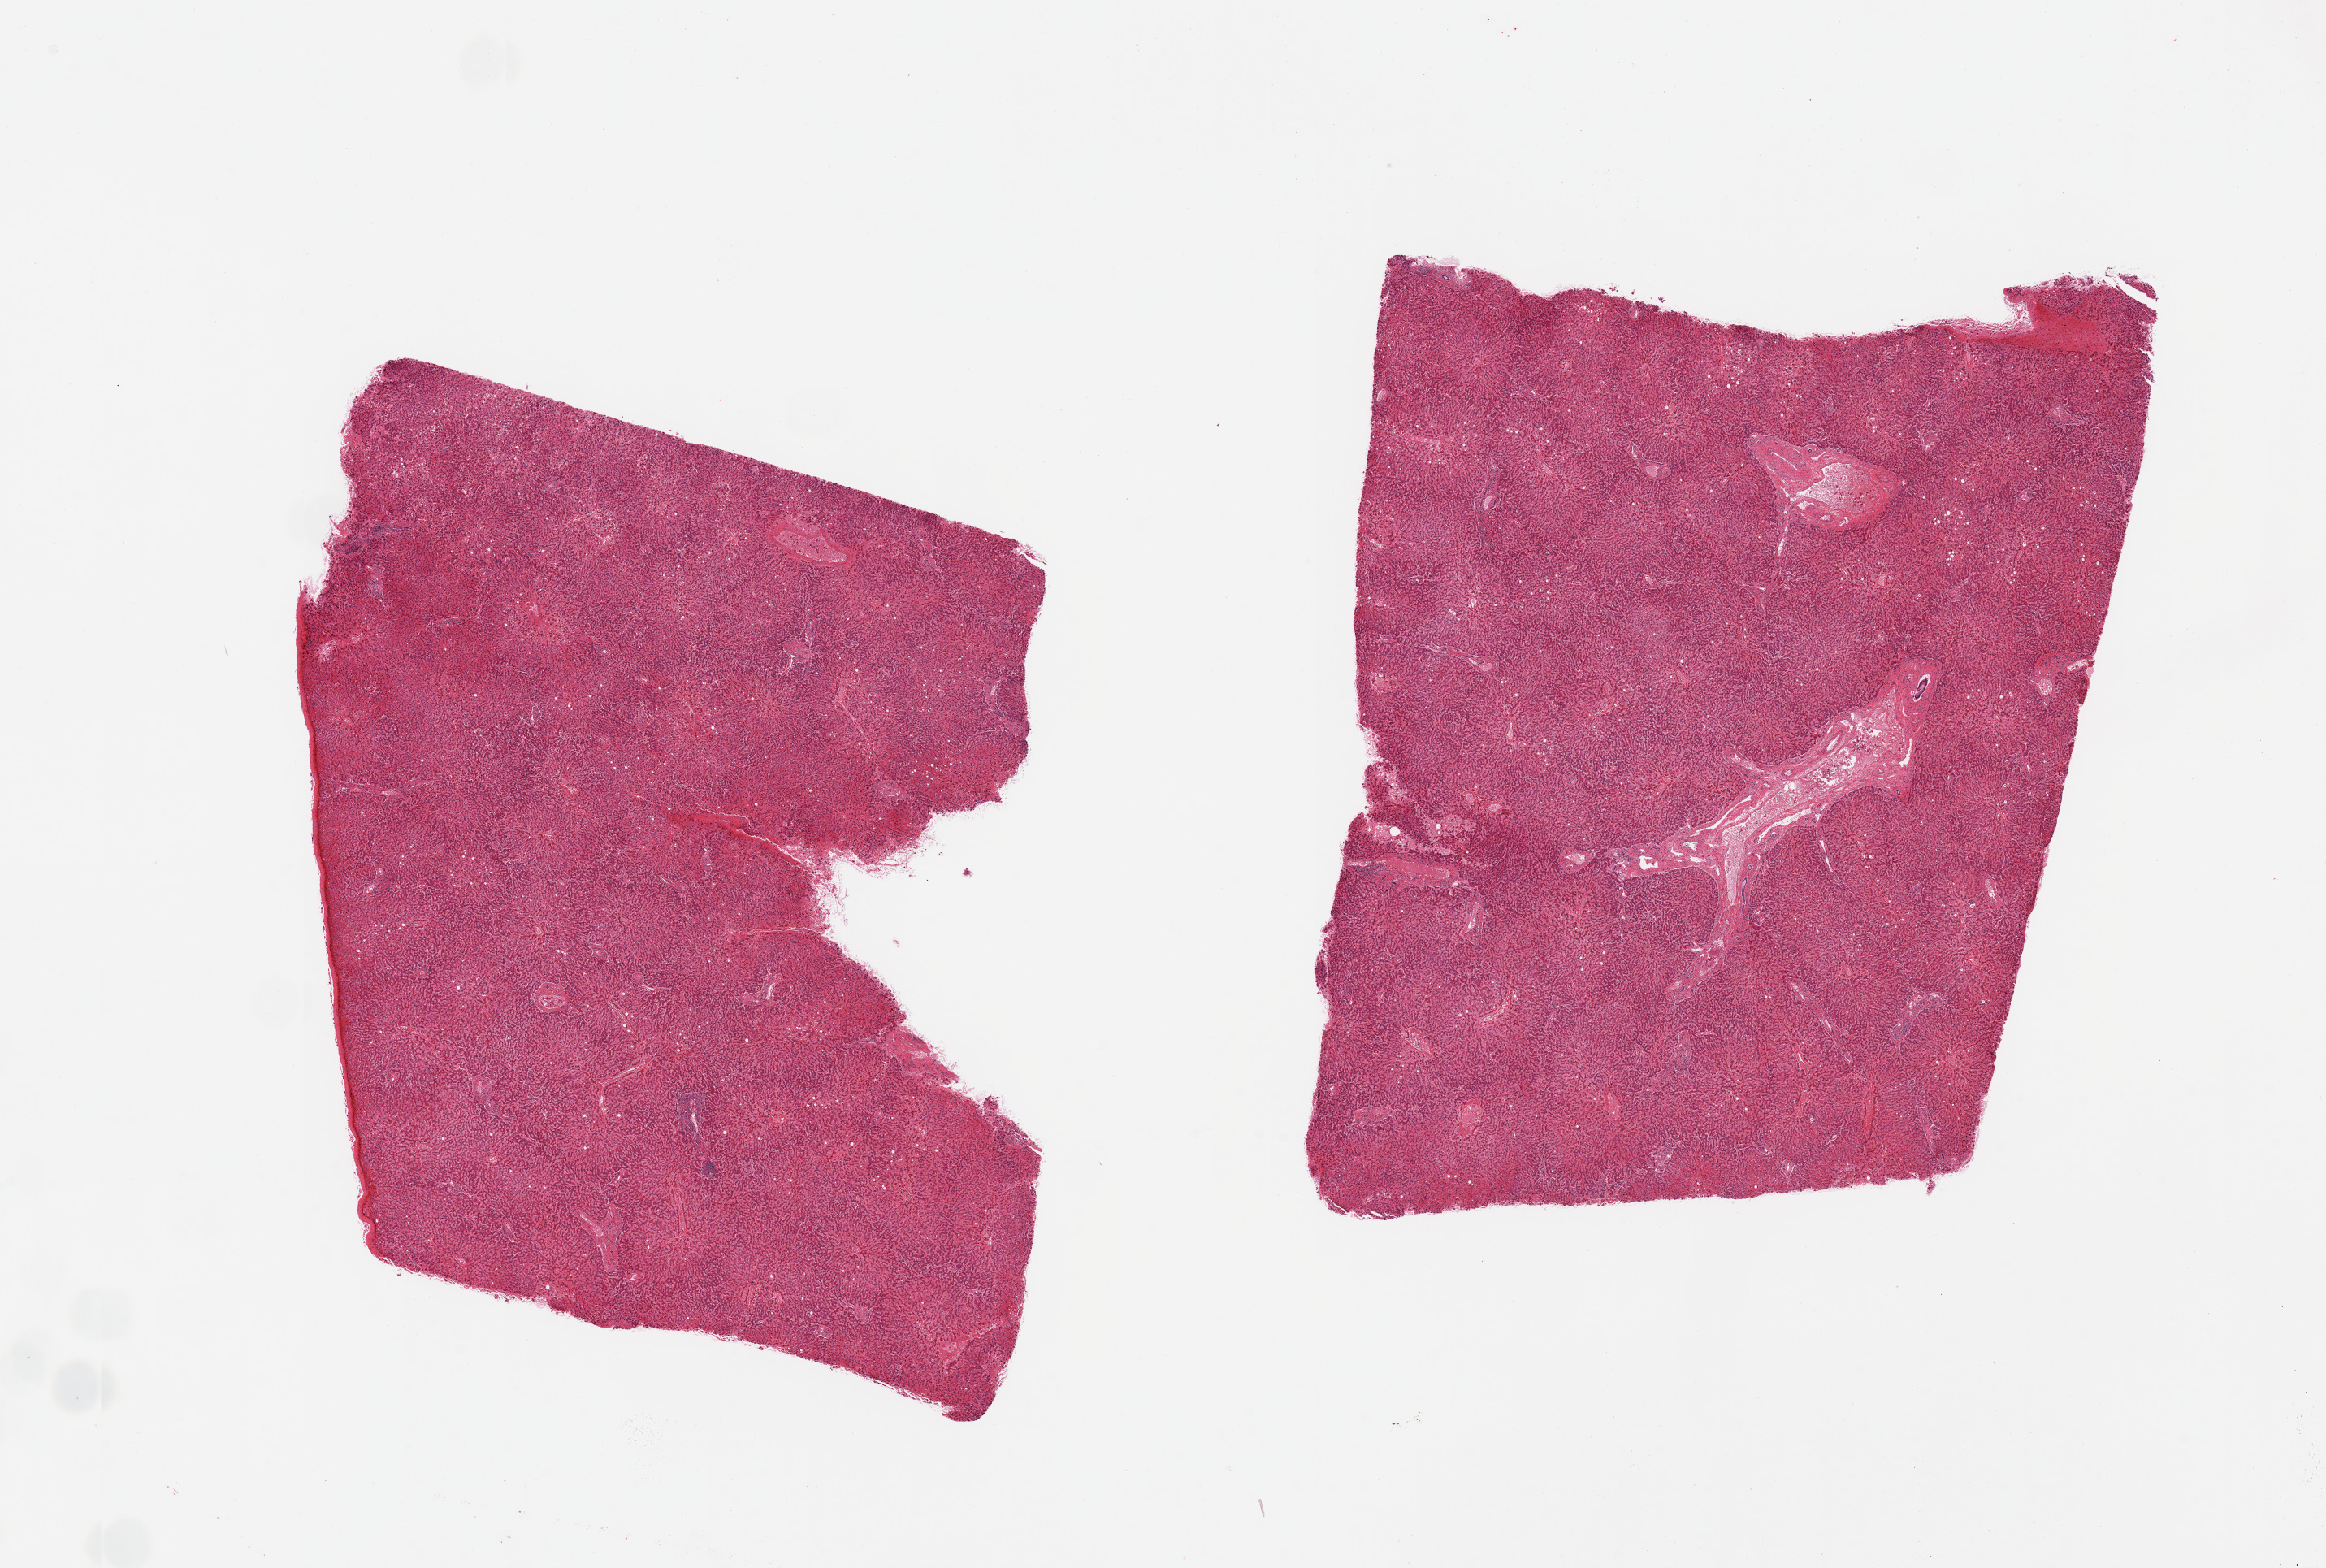
Hematoxylin and eosin (H&E) whole-slide image — shown as a low-resolution overview of the whole scanned area (about 22.6 x 15.3 mm, from a 20x scan). PAXgene-fixed paraffin-embedded (PFPE) section. Target tissue: liver. Tissue donor sample. Donor sex: male.
Pathologist's review note for this sample: 2 pieces. central congestion.